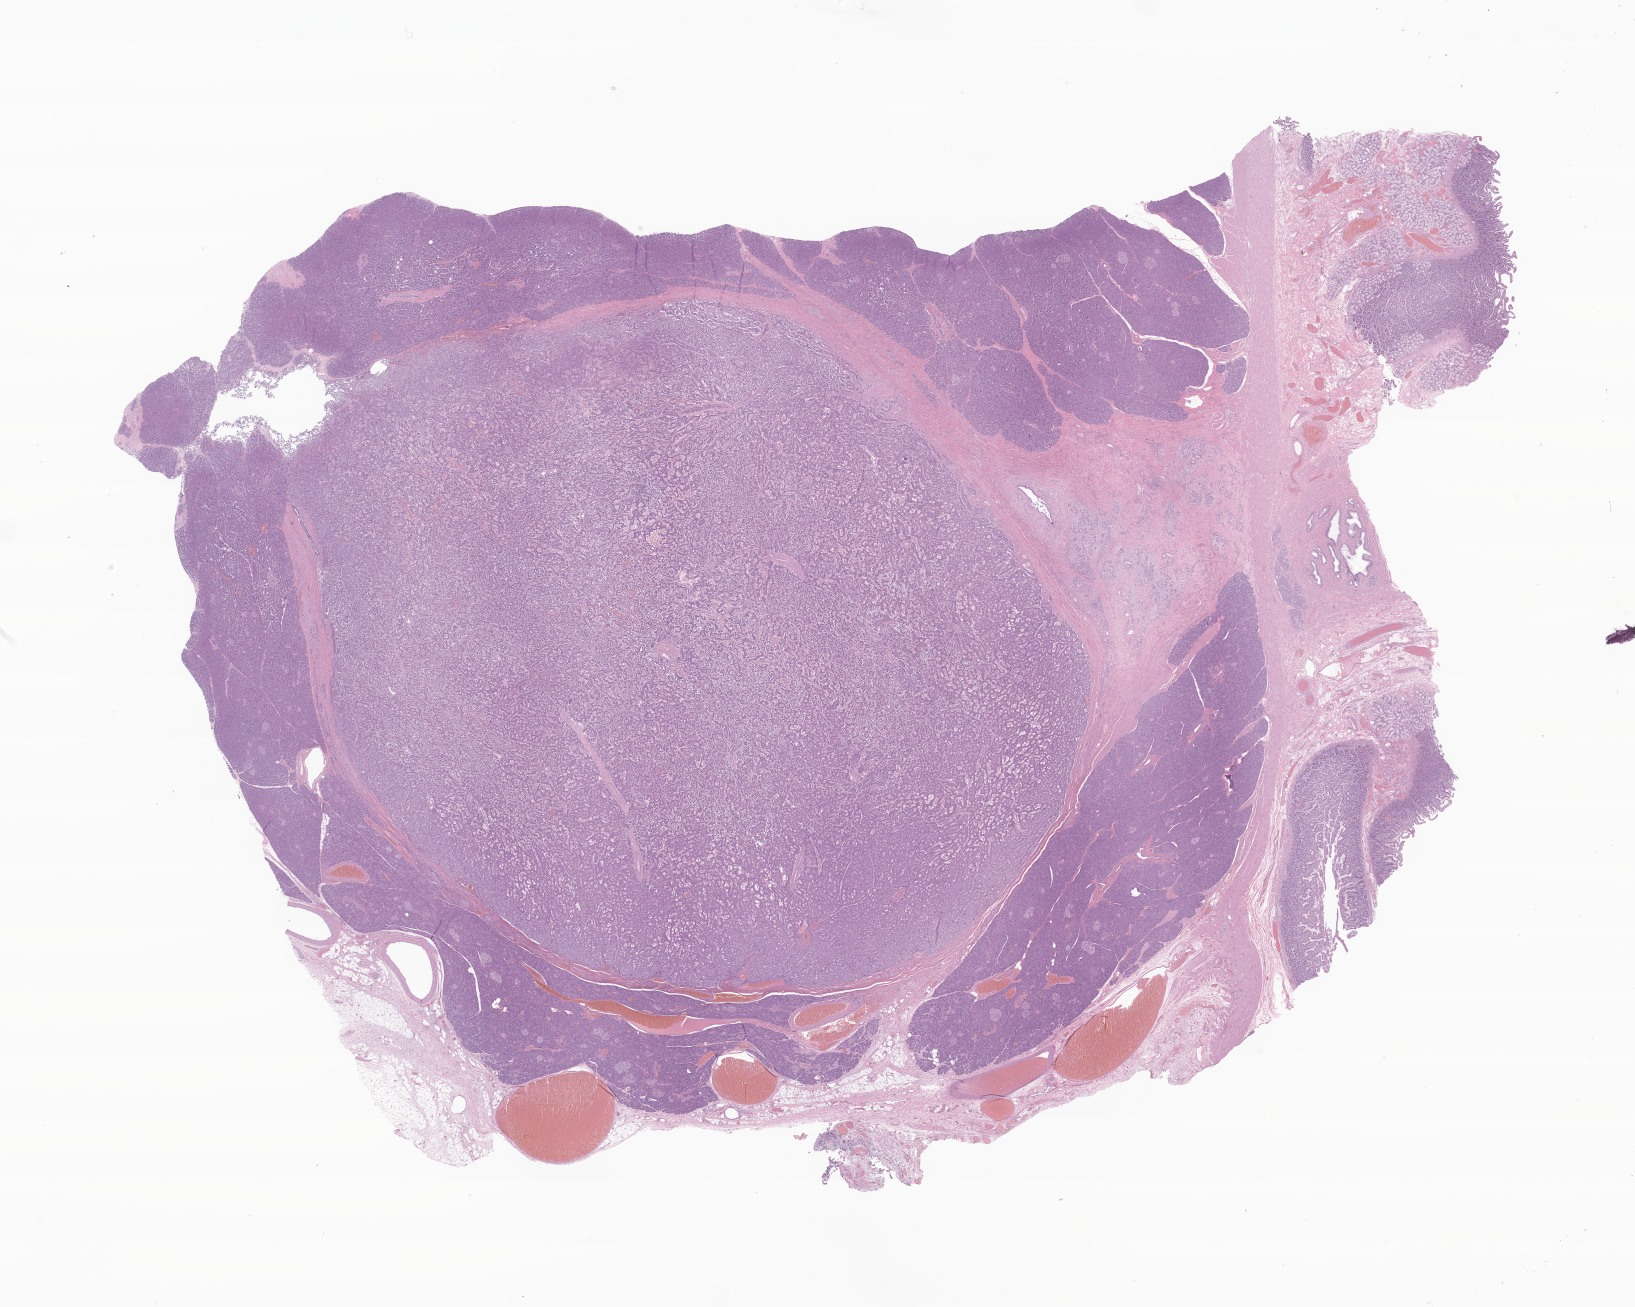
Digitized haematoxylin and eosin-stained section of tumor tissue from the head of pancreas — low-resolution overview of the scanned area, about 27.6 x 22.0 mm, formalin-fixed paraffin-embedded section. Patient: male, age 195 months (16 years 3 months).
• diagnosis (ICD-O-3 morphology term): Neuroendocrine carcinoma, NOS